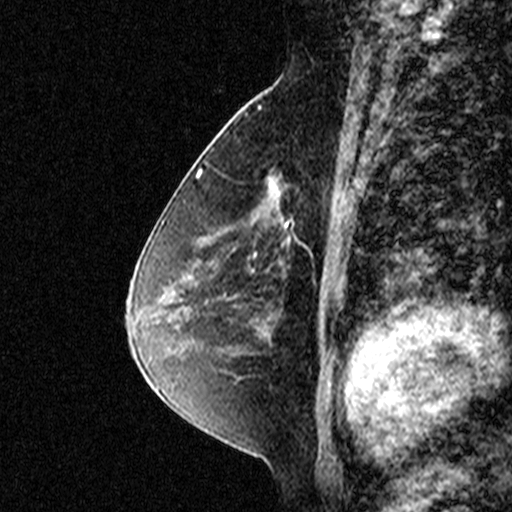
Breast MRI (dynamic contrast-enhanced), one sagittal slice. Slice 23 of 44 in the series (ordered by position). Dynamic contrast-enhanced study with each time point stored as its own series, time point 2 of 3 at this slice position (early post-contrast, ordered by acquisition time). 1.5 T. TE 4.5 ms, TR 11 ms. 512 × 512 image matrix, field of view 200 × 200 mm. Female patient, age 49 years. Case-level facts recorded for this patient, not image findings: setting: breast cancer imaged before/during neoadjuvant chemotherapy; receptor status: triple-negative.
Outlined on this slice (semi-automatically segmented with operator editing):
- analysis volume of interest (the breast-tissue region the enhancement analysis was run in; not a lesion): bounding box <238,122,331,227> (left, top, right, bottom; pixels)
- tumour enhancement mask (voxels above the 90 % enhancement threshold inside the analysis volume of interest): <270,173,294,227>